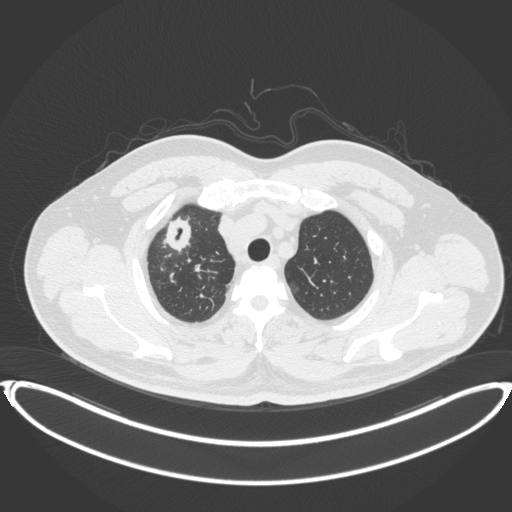
Chest CT, one axial slice. Position 329 of 399 along the scan axis. Reconstruction kernel B31f. 120 kVp. Lung window (W 1500 / L -600 HU). 1 mm slice thickness. 512 × 512 image matrix, field of view 445 × 445 mm. Male patient, age 53 years. From the clinical record (not read from this slice): clinical TNM (as recorded): T2a N0 M0.
Annotated regions visible in this slice (rectangle marked by the reading radiologist):
- lung tumour (recorded histology: adenocarcinoma): bounding box [x1, y1, x2, y2] px = [162, 212, 194, 254]